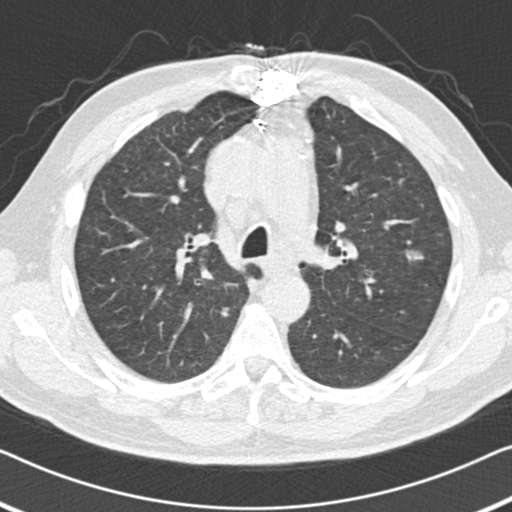
Low-dose screening chest CT, one axial slice. Slice 105 of 155 in the series (ordered by position). 120 kVp. Lung window (W 1500 / L -600 HU). 512 × 512 image matrix.
Annotated regions visible in this slice (outlined manually by an expert reader):
- lesion 1 (tumor, upper lobe of left lung): bounding box (x1, y1, x2, y2) in pixels: (405, 250, 424, 262)